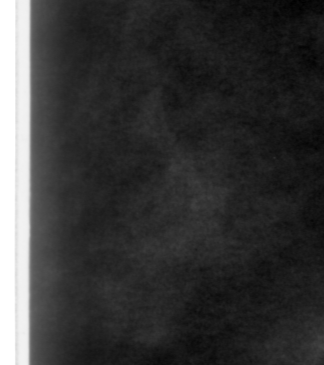
Crop from a digitized film mammogram around one marked abnormality; left breast; CC view; BI-RADS breast density category 1 (scale 1–4).
- Finding: mass, shape irregular, margins obscured; BI-RADS assessment category 0 (incomplete: needs additional imaging); pathology result (as recorded, not read from the image): benign.